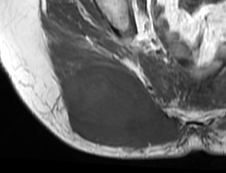
MRI of an extremity soft-tissue mass, one axial slice. Position 40 of 73 along the scan axis. MR volume resampled by the dataset authors to the PET/CT grid (not the native acquisition matrix). 3.27 mm slice thickness. 226 × 173 image matrix, field of view 221 × 169 mm. Female patient. Case-level facts recorded for this patient, not image findings: histological type: spindle cell suggestive of myxofibrosarcoma; grade: intermediate; site of the primary tumour: right buttock.
Structures marked on this image (expert contour drawn on MRI and transferred to this co-registered scan by the dataset authors):
- gross tumour volume (mass): bounding box [x1, y1, x2, y2] px = [59, 63, 183, 150]